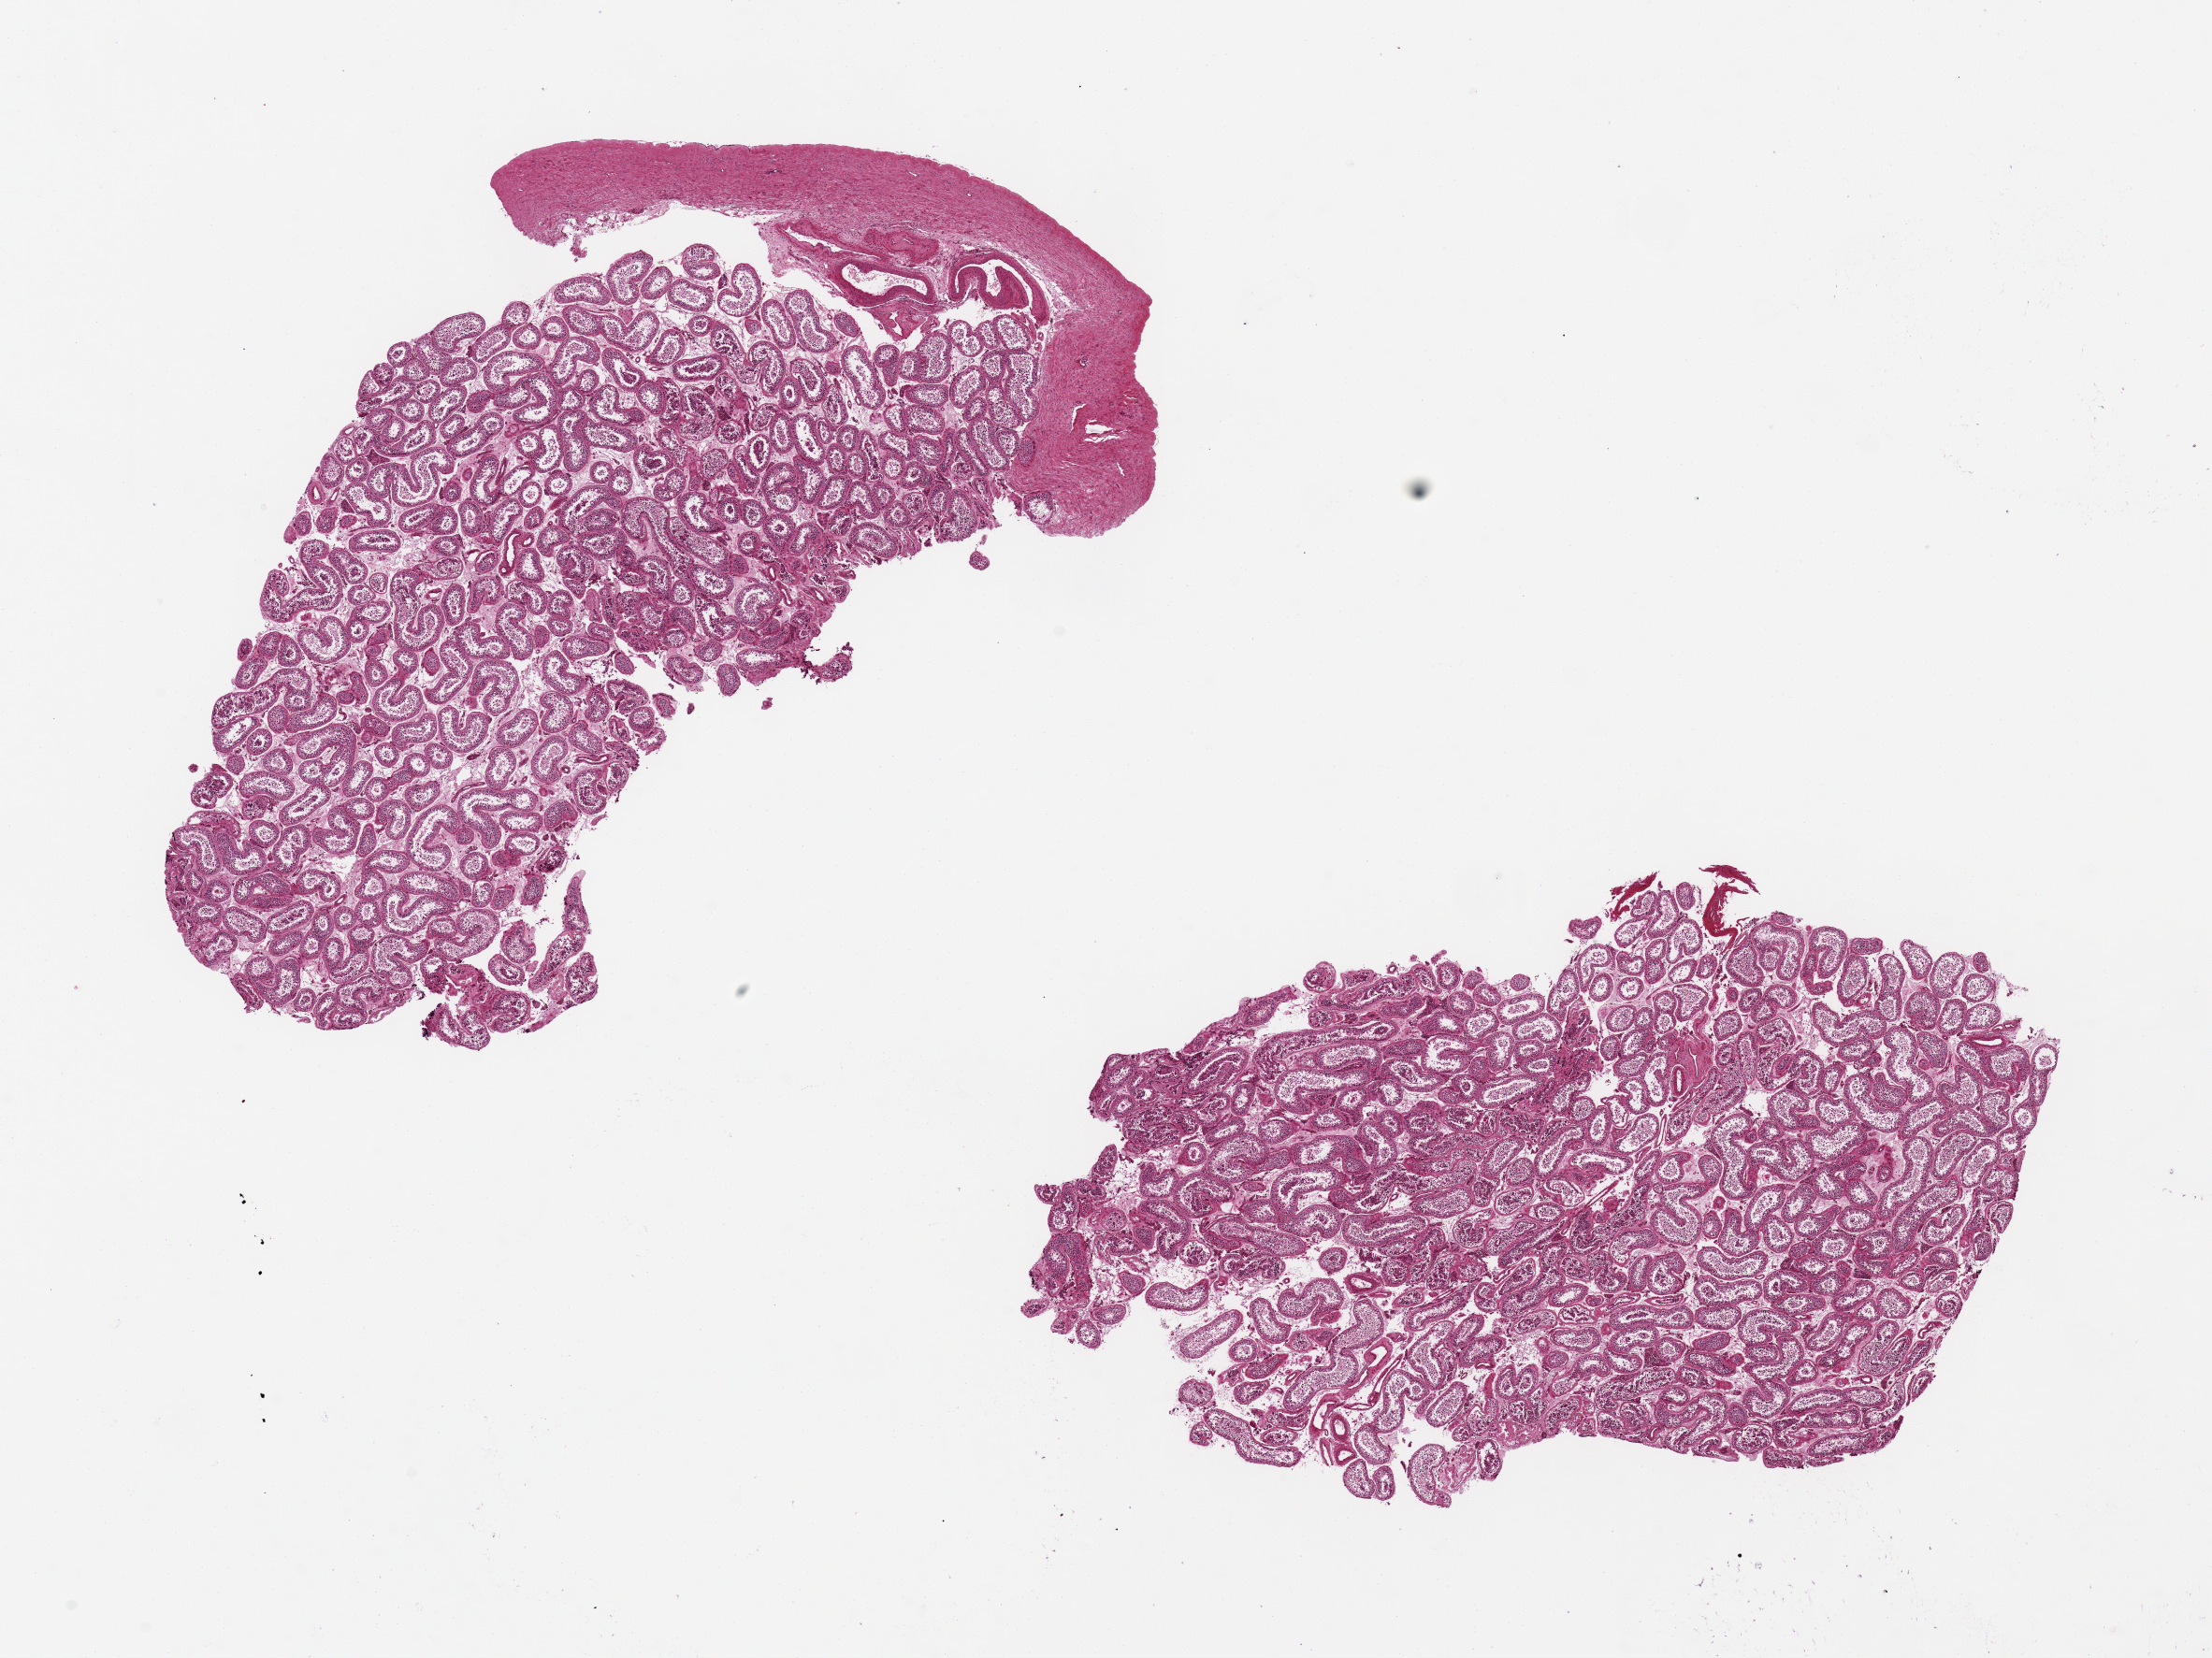
Whole-slide image, H&E stain — a low-resolution overview of the entire scanned area, about 18.7 x 14.0 mm (acquisition: 20x scan). PAXgene-fixed paraffin-embedded (PFPE) section. Sampled site (target tissue): testis. Donor tissue sample. Male donor.
• pathologist's review note for this sample: 2 pieces, ~8x5mm. Spermatogenesis is present but poorly preserved